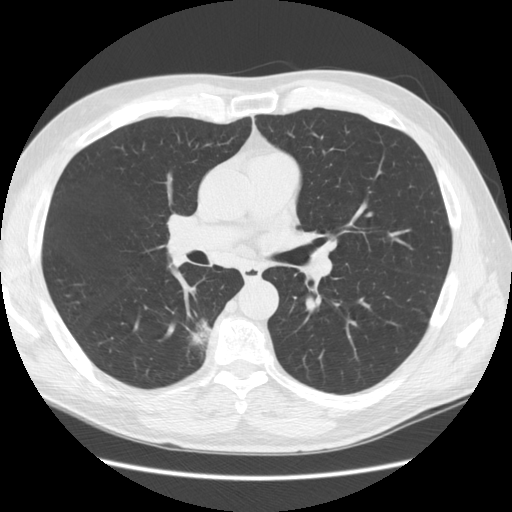
Low-dose screening chest CT, axial slice, second screening round (one year after baseline), lung window (W 1500 / L -600 HU), 2.5 mm slice thickness, 512 × 512 image matrix. Male, age 69 years at enrolment. Former smoker at enrolment.
Lesion marked by an expert reader, bounding box [x1, y1, x2, y2] px = [169, 306, 227, 361]. The screening reader recorded 2 non-calcified nodules or masses ≥4 mm on this exam (right lower lobe, right middle lobe); which of them this box marks is not recorded. Official screen result: positive, other. Participant outcome: lung cancer diagnosed 88 days after this screen — bronchiolo-alveolar adenocarcinoma, NOS, right lower lobe, well differentiated (G1), stage IB (AJCC 6th edition), 23 mm at pathology.